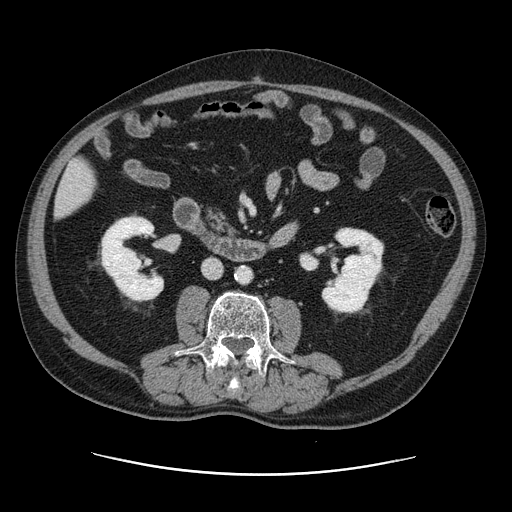
Contrast-enhanced abdominal CT, one axial slice; position 32 of 141 along the scan axis; 120 kVp; soft-tissue window (W 400 / L 40 HU); 512 × 512 image matrix, field of view 395 × 395 mm. Male patient, age 72 years. Case-level facts recorded for this patient, not image findings: diagnosis: colorectal cancer liver metastases, imaged before liver resection; multiple liver metastases: yes; largest metastasis: 5.4 cm; disease in both lobes: yes.
Outlined on this slice (manually delineated by an expert):
- liver: bounding box <57,160,96,216> (left, top, right, bottom; pixels)
- planned liver remnant (the part of the liver to remain after resection): <57,160,96,216>